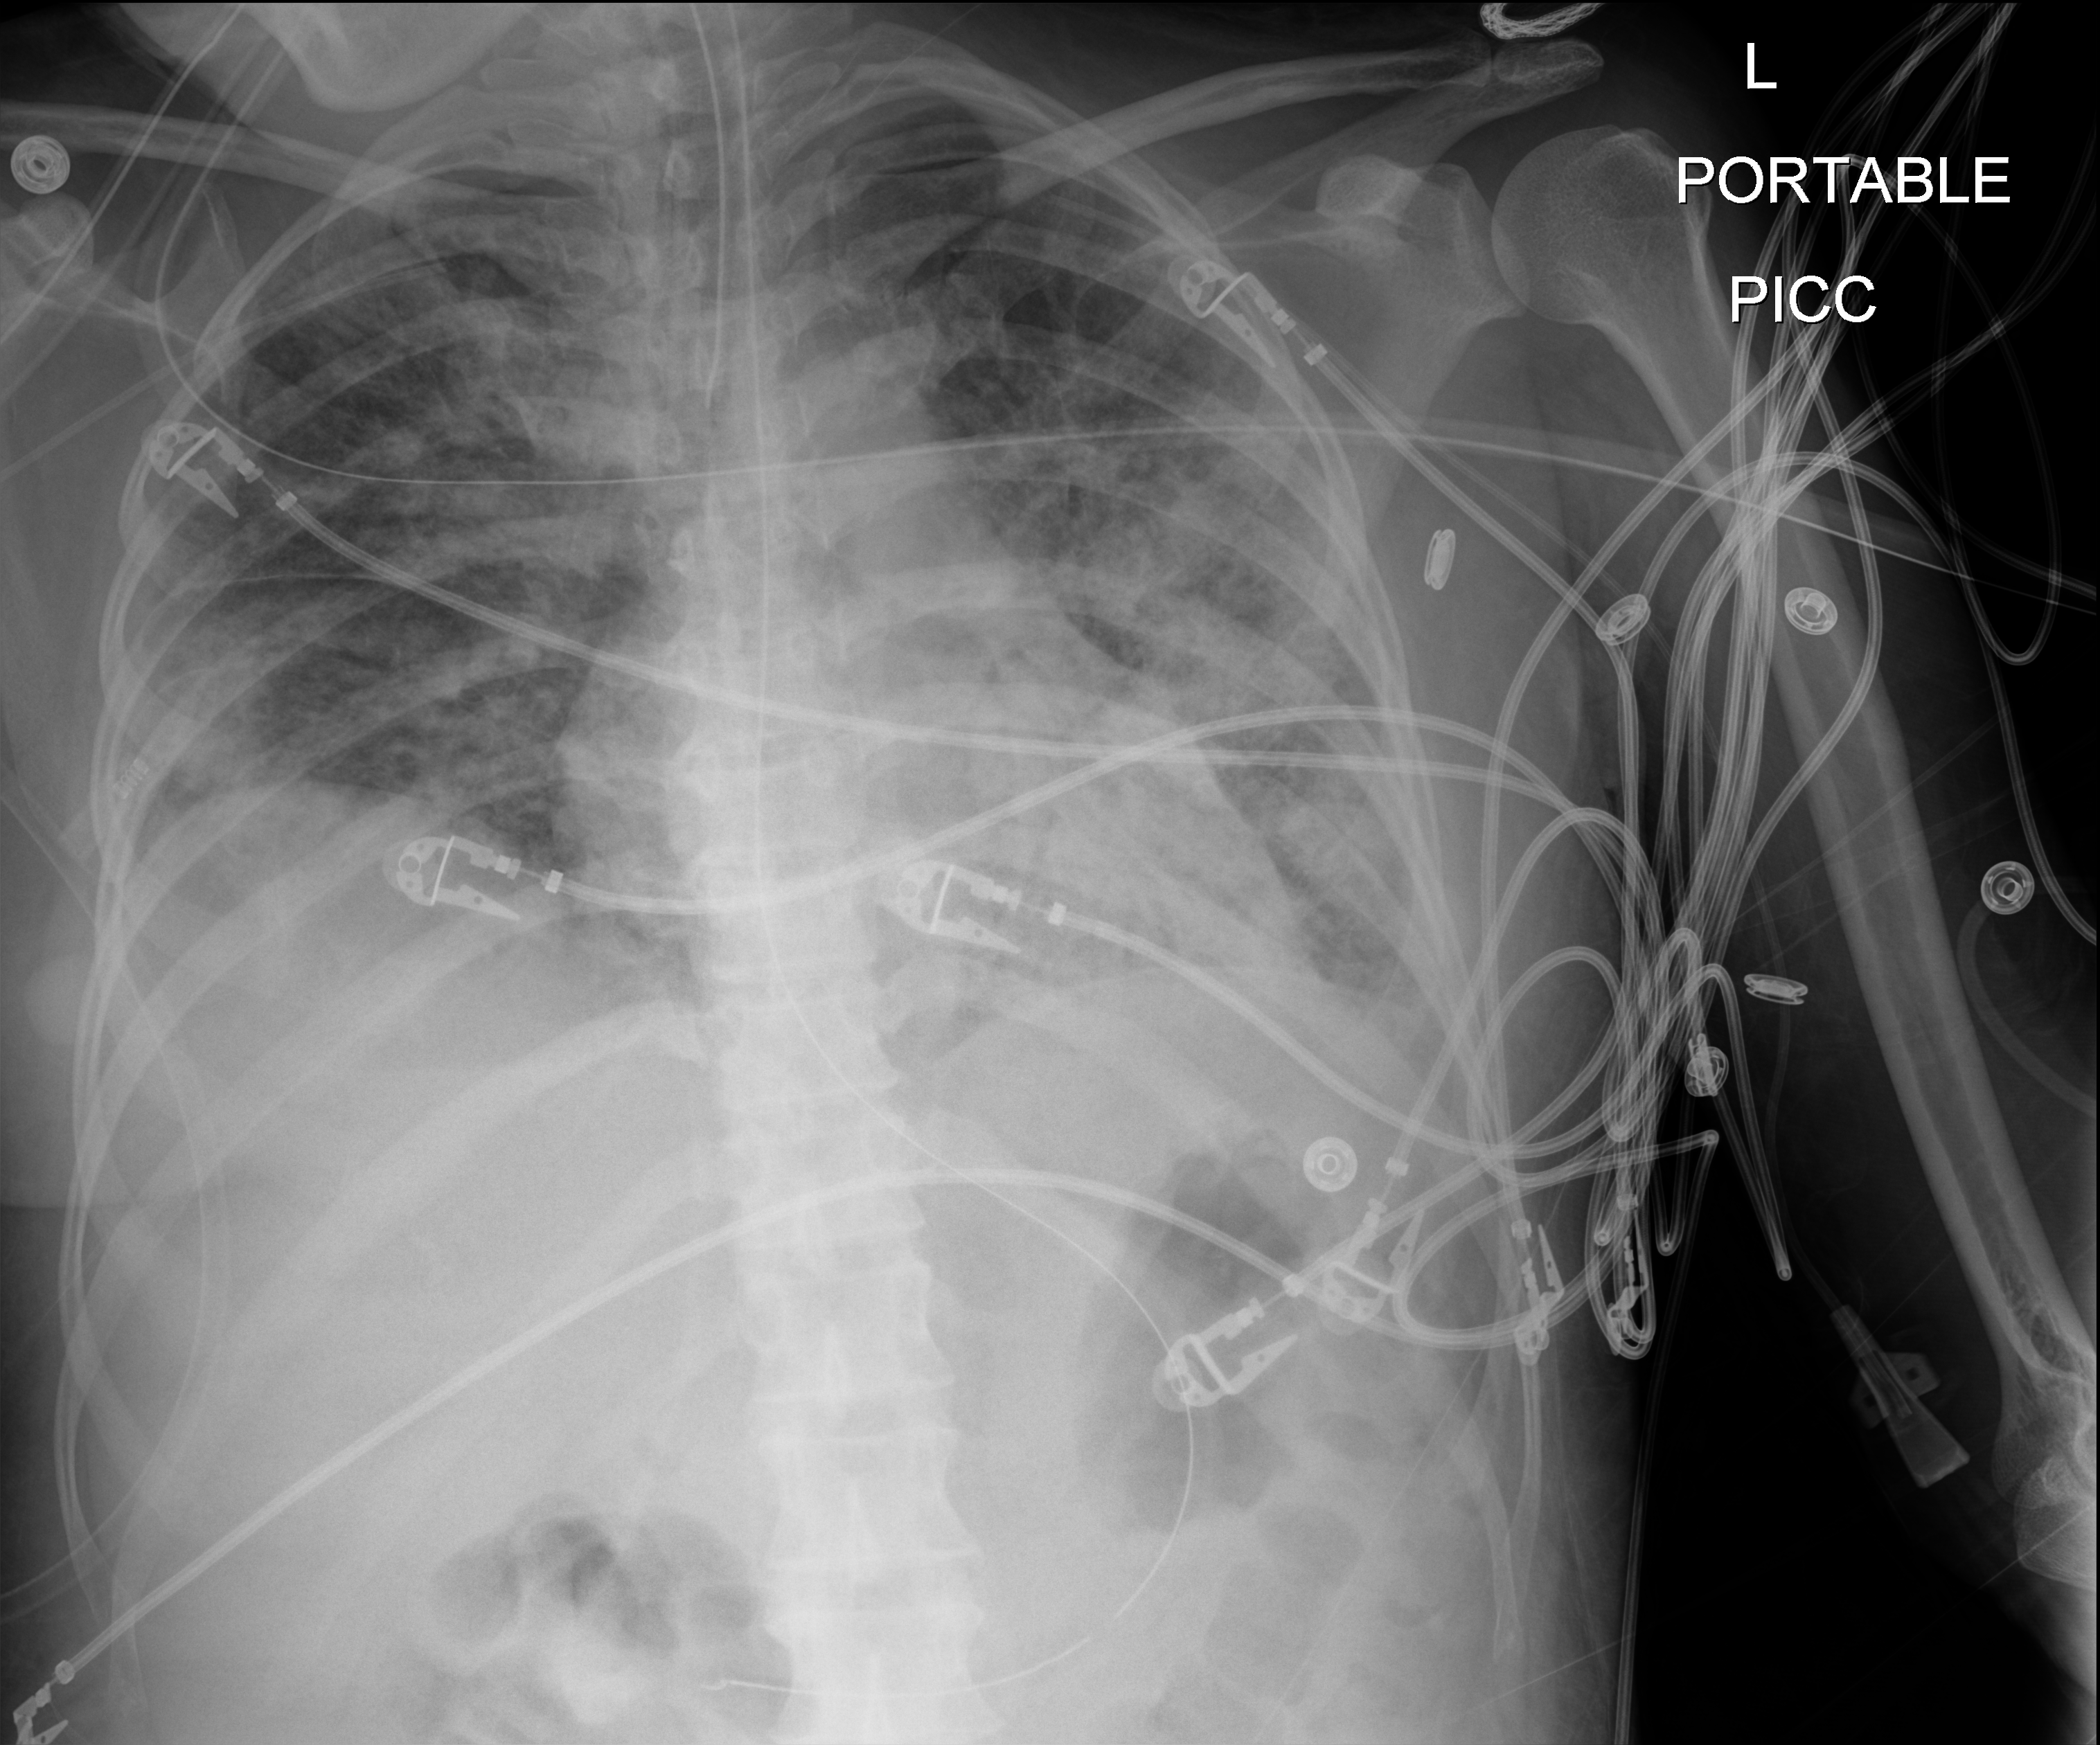
Bedside chest radiograph (digital radiography). Patient hospitalised with COVID-19; female, aged 18–59 years.
Hospital-stay facts (about this admission, not read from this image; timing relative to this image not recorded): mechanically ventilated during this hospital stay: yes.